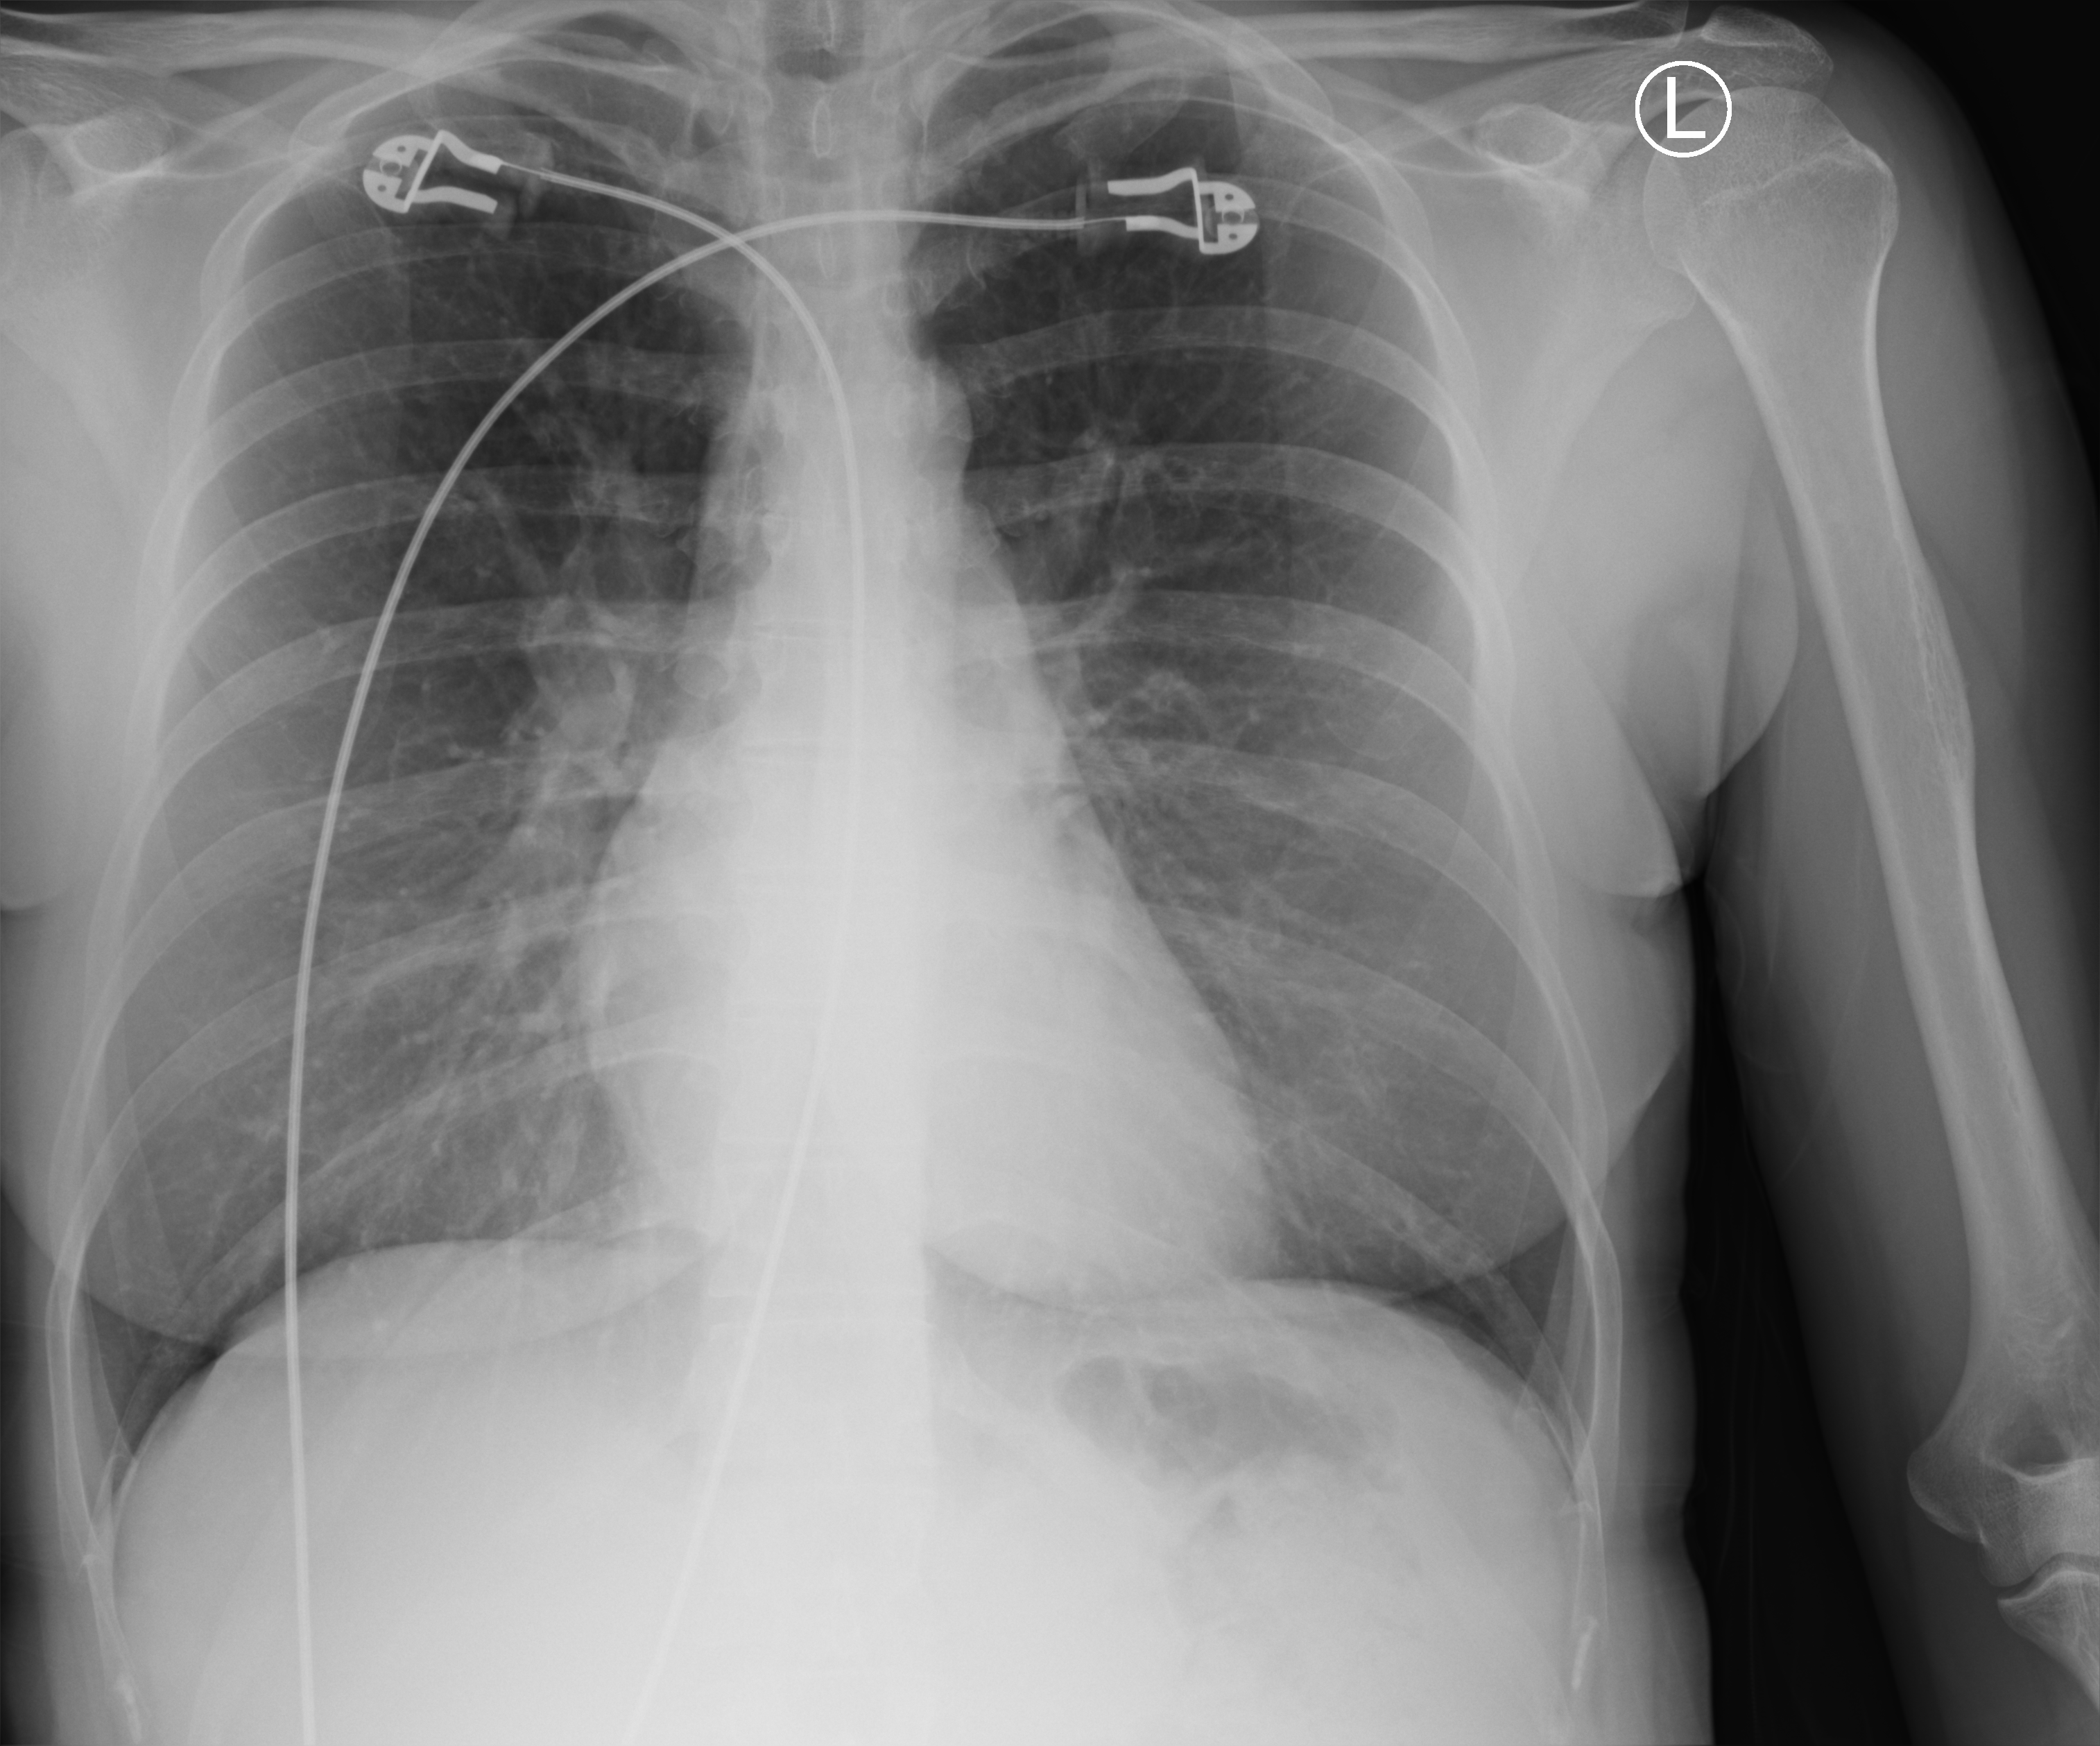
Bedside chest radiograph (computed radiography); anteroposterior (AP) projection. Female patient hospitalised with COVID-19, age 18–59 years.
From the hospital-stay record, not from the radiograph (when in the stay this image was taken is not recorded):
- other chronic lung disease (admission record): yes